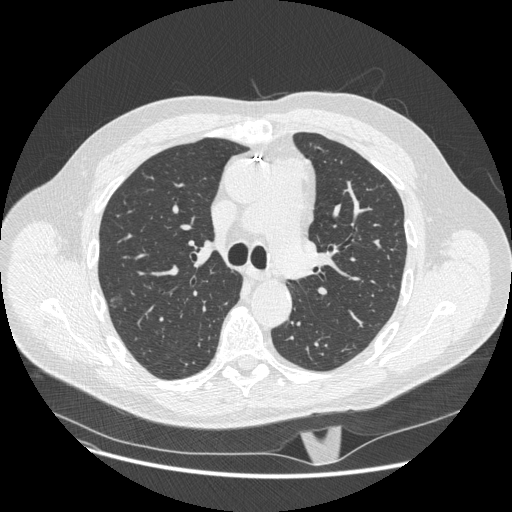
Axial slice from a low-dose chest CT screening exam, second screening round (one year after baseline), lung window (W 1500 / L -600 HU), standard (soft-tissue) reconstruction kernel (STANDARD), 120 kVp. Male participant, aged 62 years at enrolment. Current smoker at enrolment.
Lesion marked by an expert reader, box from (x=95, y=287) to (x=133, y=318) px. Reader record for this screening exam (exam-level; its link to the box is not recorded): non-calcified nodule or mass ≥4 mm, right upper lobe, 11 × 7 mm, smooth margins, pre-existing on the prior screen: yes. Lung cancer was diagnosed 482 days after this screen: adenocarcinoma, NOS, right upper lobe, moderately differentiated (G2), stage IA (AJCC 6th edition), 12 mm at pathology.